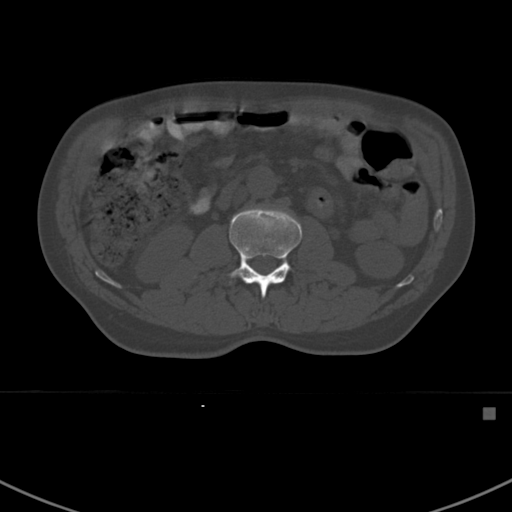
CT including the spine, one axial slice; position 285 of 412 along the scan axis; reconstruction kernel Br40s; 120 kVp; bone window (W 1800 / L 400 HU); 1.5 mm slice thickness; 512 × 512 image matrix, field of view 358 × 358 mm. Male patient, age 59 years. From the clinical record (not read from this slice): primary cancer: prostate.
Annotated regions visible in this slice (semi-automatically segmented with operator editing):
- L2 vertebra: bounding box <228,207,302,299> (left, top, right, bottom; pixels)